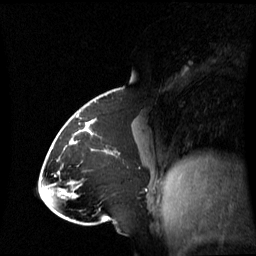
Breast MRI (dynamic contrast-enhanced), one sagittal slice. Slice 29 of 60 in the series (ordered by position). Dynamic contrast-enhanced series, image 2 of 3 at this slice position (ordered by acquisition). 1.5 T. TE 4.2 ms, TR 8.4 ms. 2.8 mm slice thickness. 256 × 256 image matrix, field of view 270 × 270 mm. Patient: female, 43 years. From the clinical record (not read from this slice): setting: breast cancer imaged before/during neoadjuvant chemotherapy; receptor status: triple-negative.
Outlined on this slice (semi-automatic segmentation, software-assisted and operator-edited):
- analysis volume of interest (the breast-tissue region the enhancement analysis was run in; not a lesion): bounding box [x1, y1, x2, y2] px = [65, 118, 143, 198]
- tumour enhancement mask (voxels above the 70 % enhancement threshold inside the analysis volume of interest): [76, 121, 94, 143]